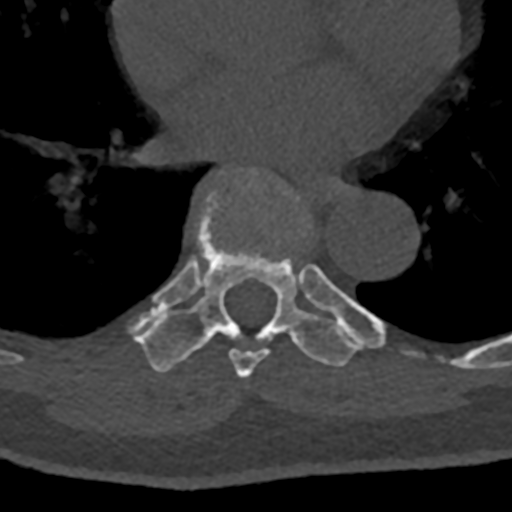
CT including the spine, one axial slice; reconstruction kernel Br40s/3; 120 kVp; bone window (W 1800 / L 400 HU); 0.5 mm slice thickness; 512 × 512 image matrix, field of view 160 × 160 mm. Male patient, age 74 years. Case-level facts recorded for this patient, not image findings: primary cancer: renal; vertebrae with lytic lesions (as recorded): T10, L1, L2, L3, L4, L5.
Outlined on this slice (semi-automatically segmented with operator editing):
- T7 vertebra: bounding box <210,167,352,378> (left, top, right, bottom; pixels)
- T8 vertebra: <133,191,384,372>